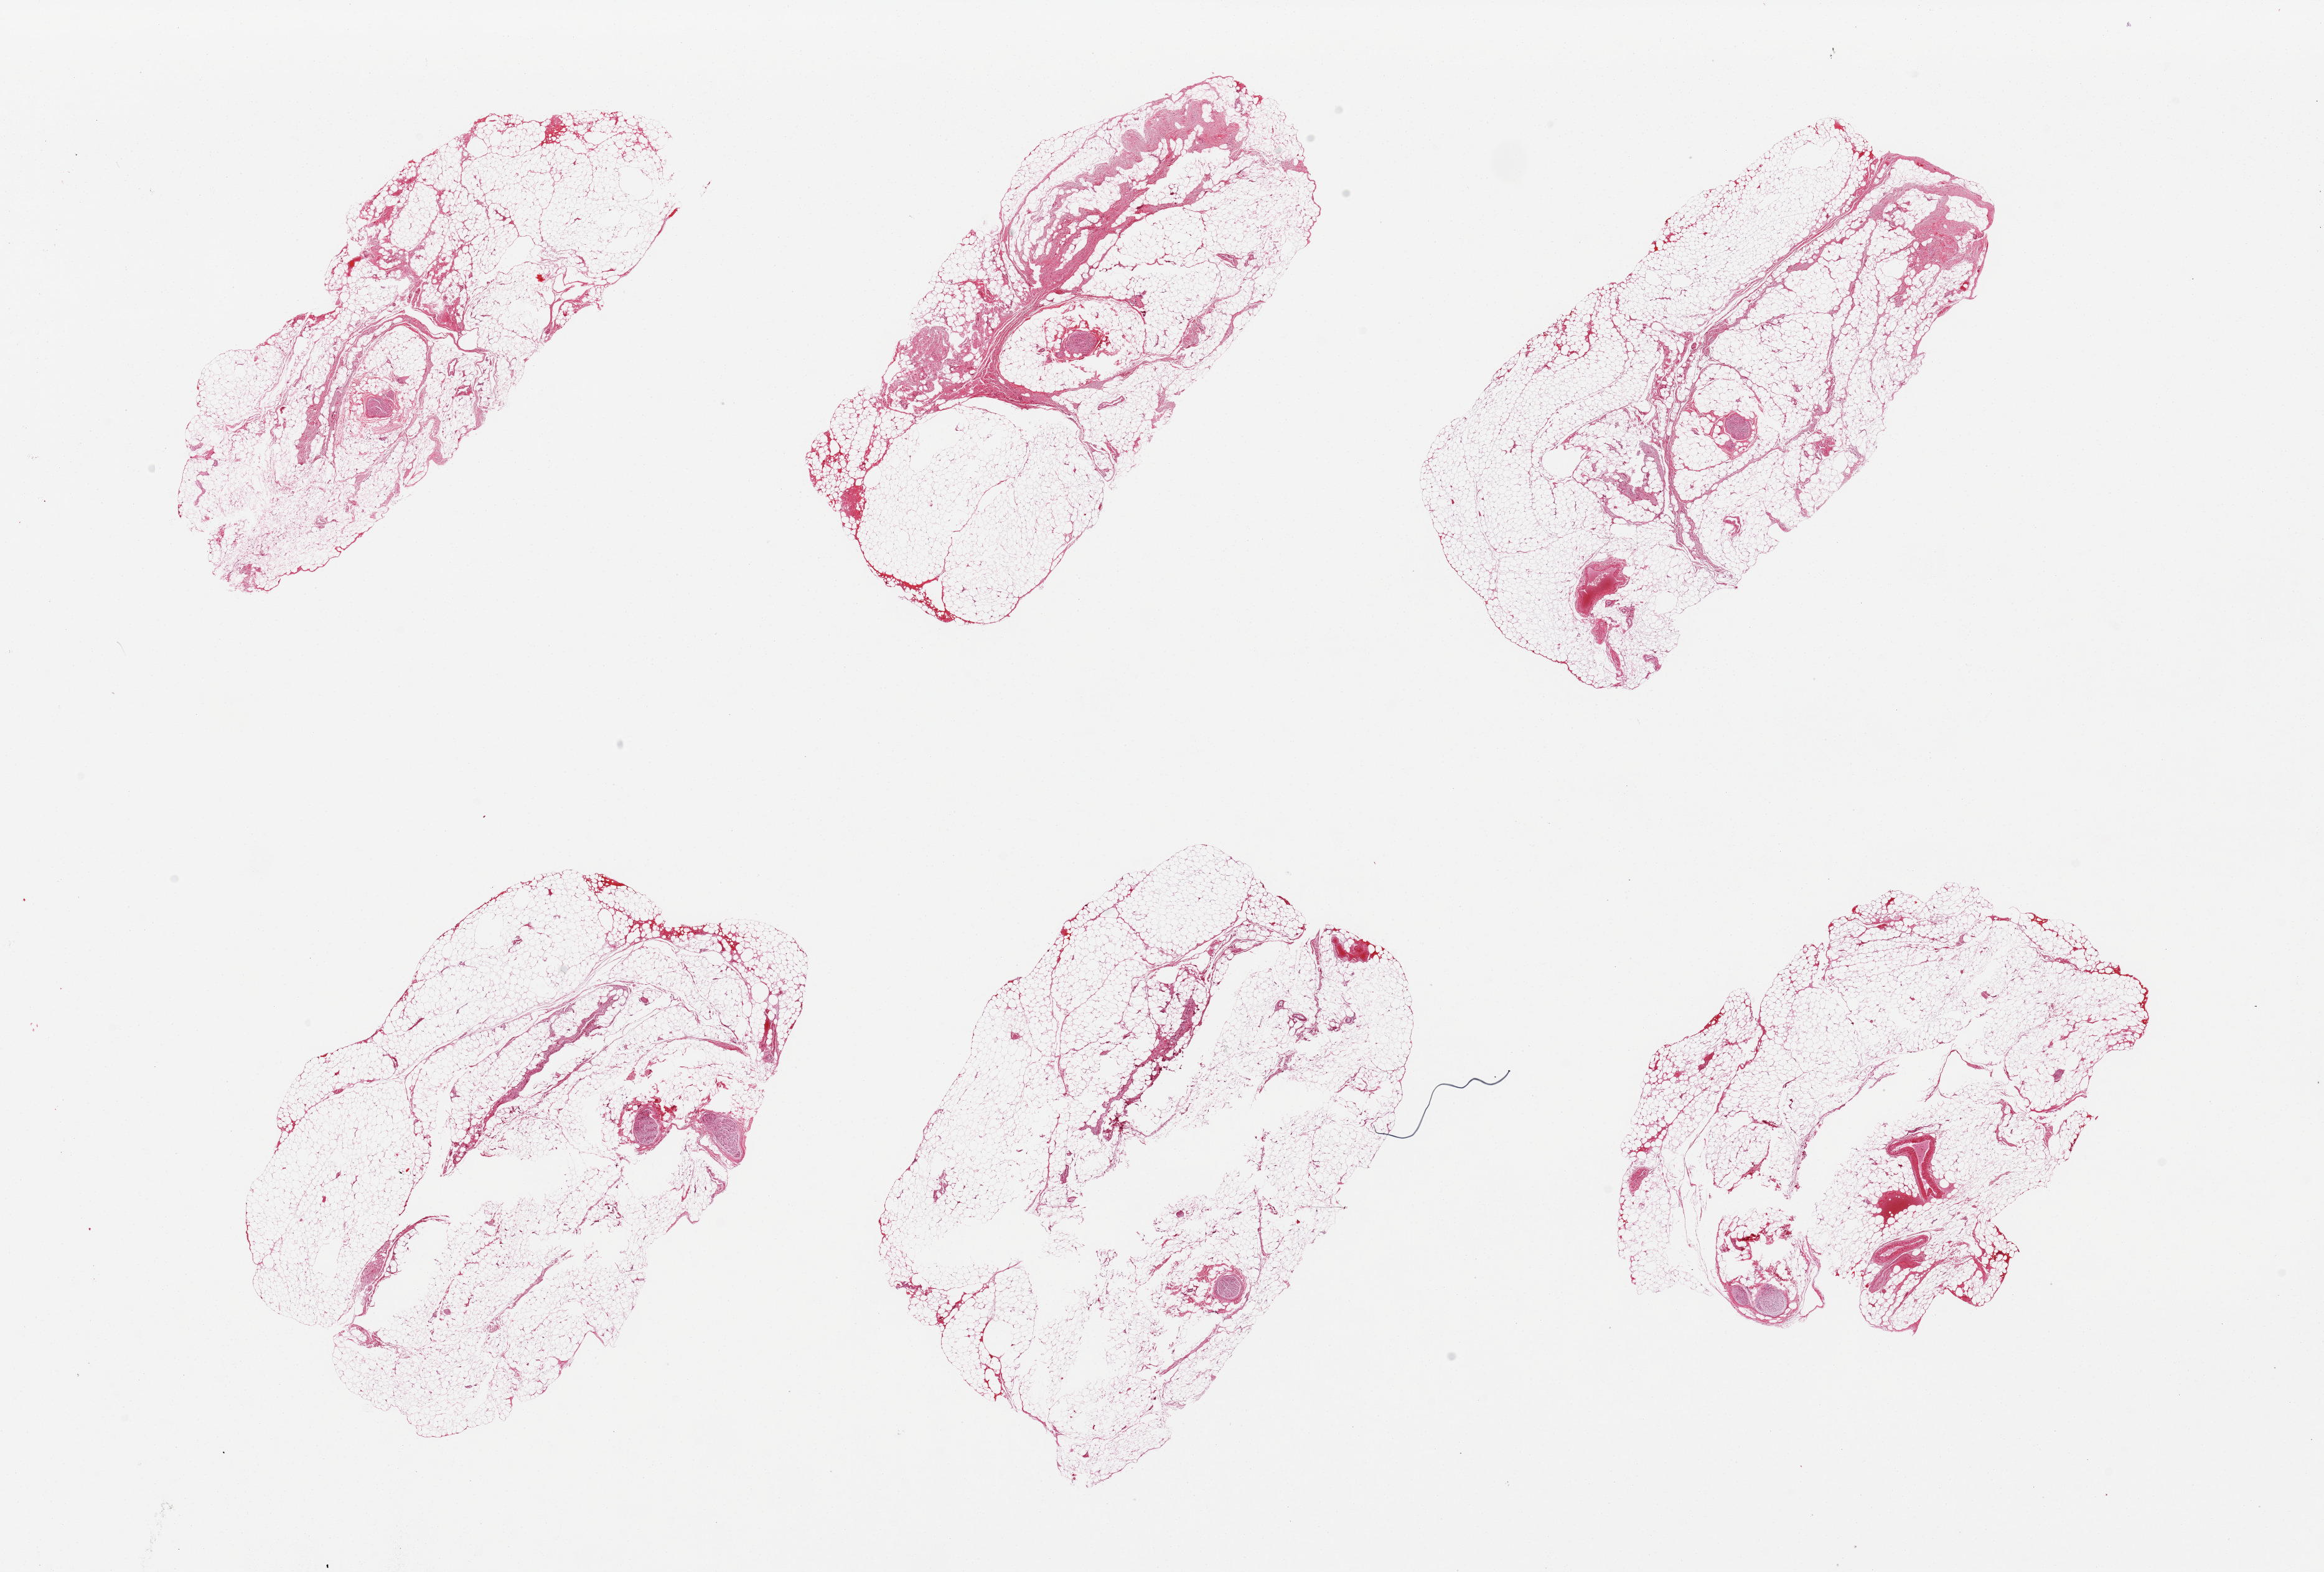
Digitized hematoxylin and eosin (H&E)-stained section, brightfield — low-resolution overview of the scanned area, about 29.5 x 20.0 mm (acquisition: 20x scan). PAXgene-fixed paraffin-embedded (PFPE) section. Section of gastroesophageal junction (target tissue). Tissue donor sample.
Review note (as recorded): 6 pieces, predominantly fat and small portion of nerve.